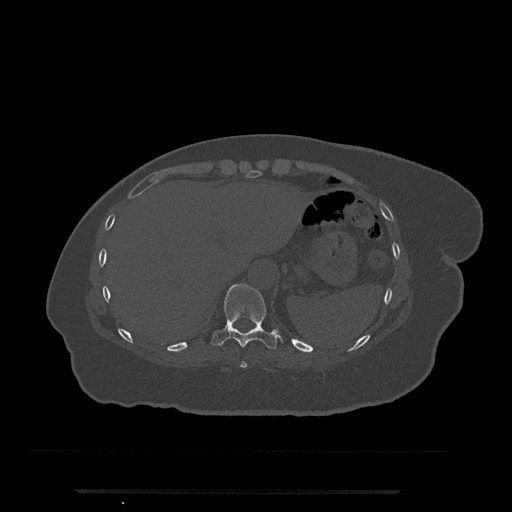
CT including the spine, one axial slice. Slice 288 of 797 in the series (ordered by position). 120 kVp. Bone window (W 1800 / L 400 HU). 0.5 mm slice thickness. 512 × 512 image matrix, field of view 440 × 440 mm. Patient: female, 51 years. From the clinical record (not read from this slice): primary cancer: neuro; vertebrae with lytic lesions (as recorded): T8.
Annotated regions visible in this slice (semi-automatic segmentation, software-assisted and operator-edited):
- T10 vertebra: bounding box [x1, y1, x2, y2] px = [211, 284, 279, 349]
- T9 vertebra: [240, 361, 247, 368]